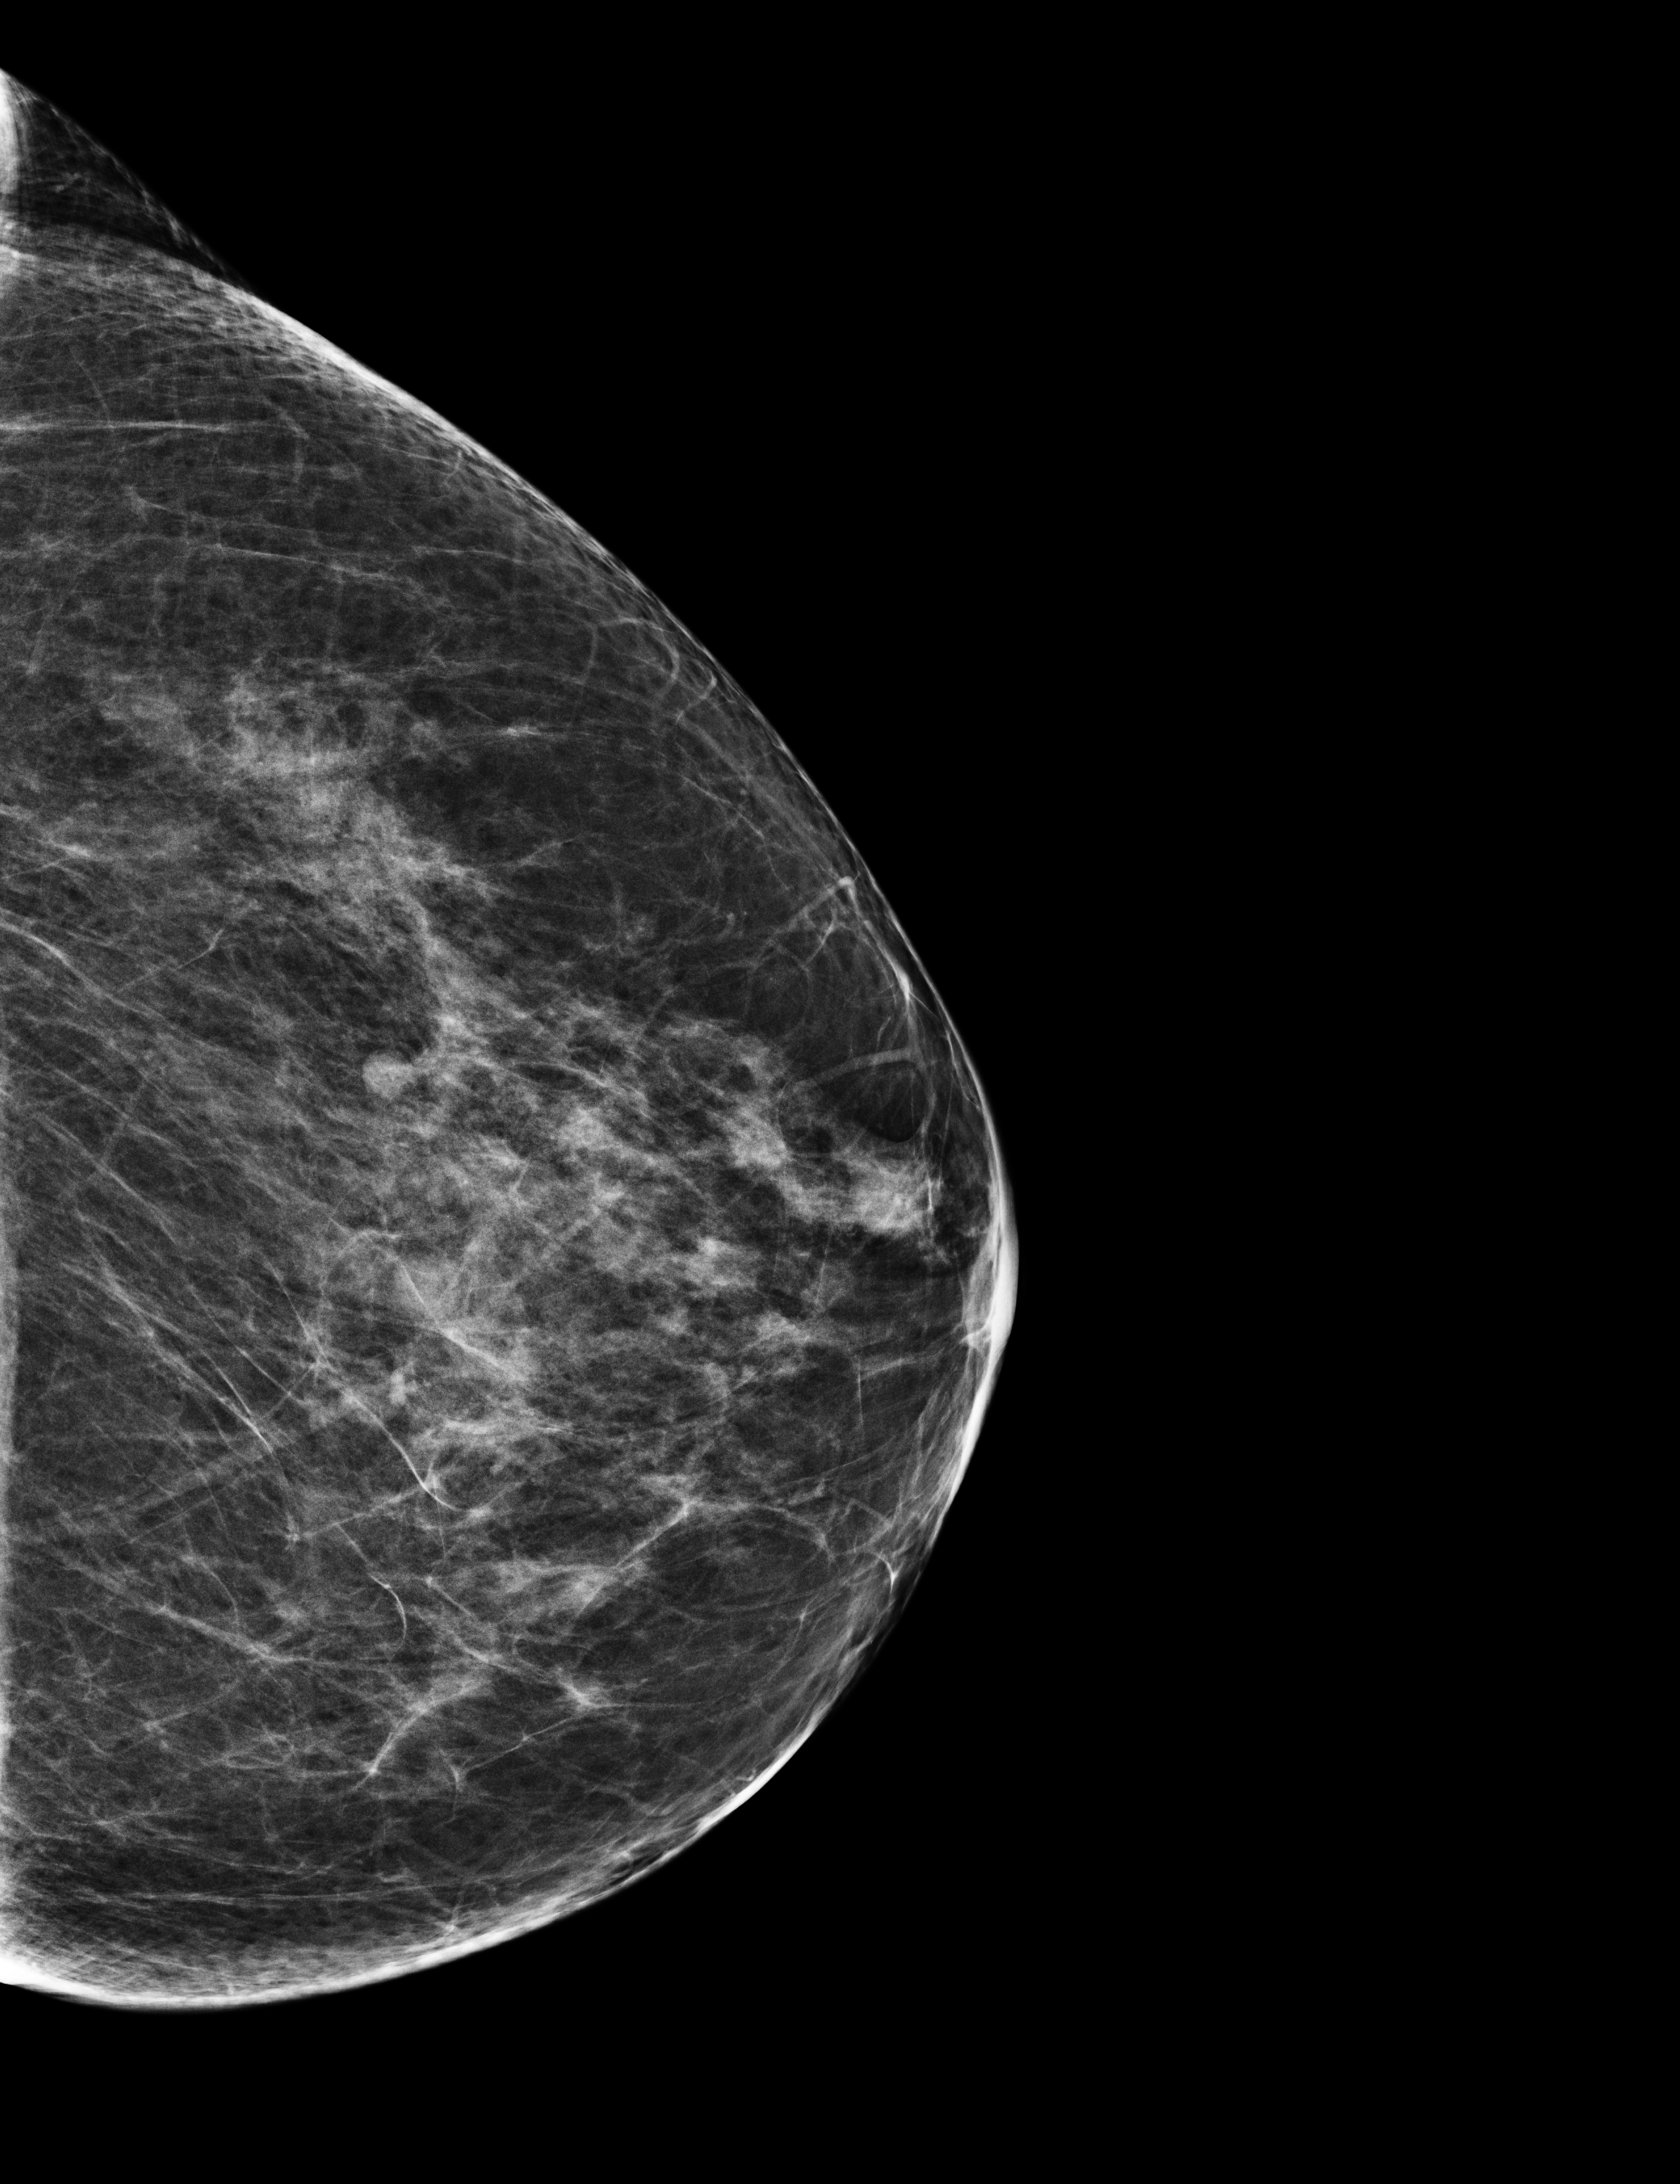
Digital mammogram (FFDM); left breast; cranio-caudal projection; screening examination; compressed breast thickness 56 mm. Female patient, age 67 years.
- breast density at the screening exam (both breasts): heterogeneously dense (BI-RADS density category c)
- final BI-RADS assessment for this screening round (tomosynthesis exam, both breasts): category 2
- recall: no recall after this screen